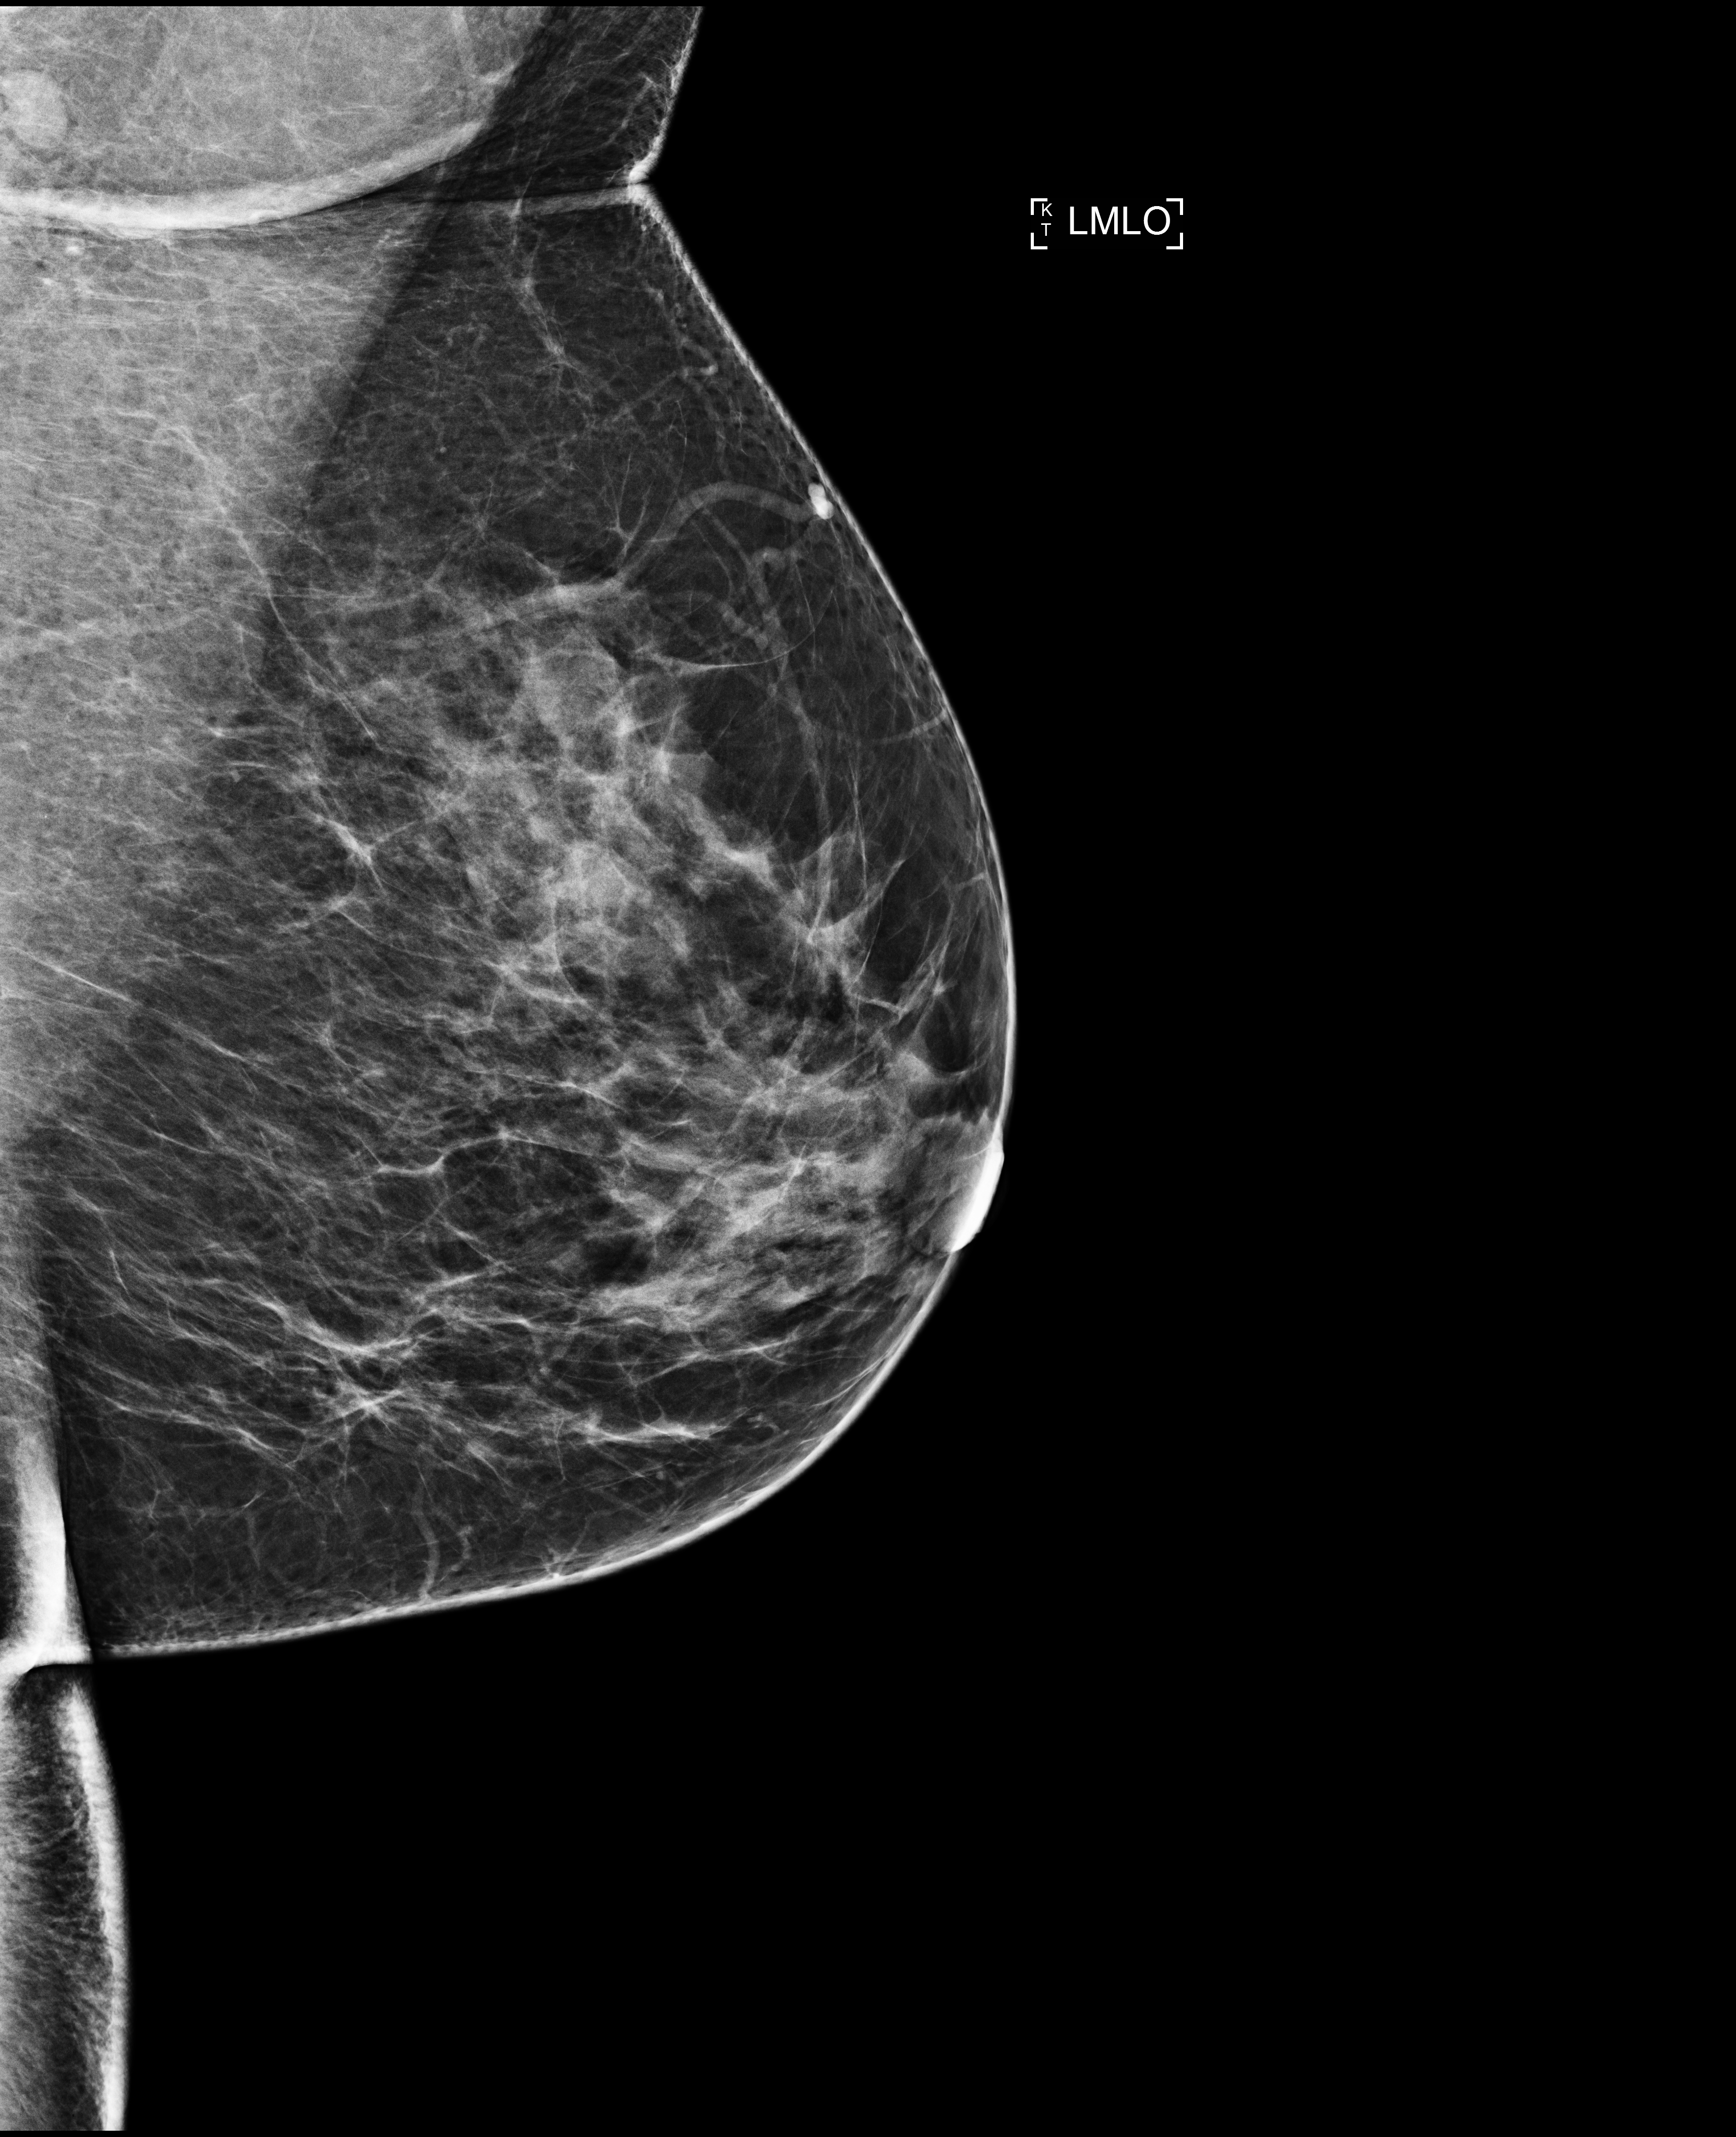
Screening examination, compressed breast thickness 67 mm. Patient: female, 54 years.
Image type: full-field digital mammogram. Breast: left. Projection: medio-lateral oblique projection.